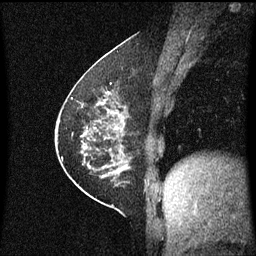
Breast MRI (dynamic contrast-enhanced), one sagittal slice. Position 28 of 60 along the scan axis. Dynamic contrast-enhanced series, image 2 of 3 at this slice position (ordered by acquisition). 1.5 T. TE 4.2 ms, TR 8.4 ms. 256 × 256 image matrix, field of view 200 × 200 mm. Patient: female, 60 years.
Outlined on this slice (semi-automatically segmented with operator editing):
- analysis volume of interest (the breast-tissue region the enhancement analysis was run in; not a lesion): bounding box (x1, y1, x2, y2) in pixels: (69, 66, 140, 193)
- tumour enhancement mask (voxels above the 70 % enhancement threshold inside the analysis volume of interest): (69, 70, 128, 177)